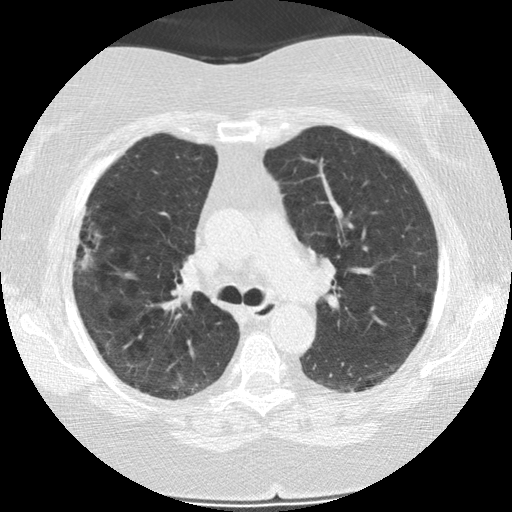
Low-dose screening chest CT, axial slice. Baseline screening round. Lung window (W 1500 / L -600 HU). 2.5 mm slice thickness. Standard (soft-tissue) reconstruction kernel (STANDARD). Slice 69 of 187 in the series. 512 × 512 image matrix. Female participant, aged 73 years at enrolment. Former smoker at enrolment.
Lesion marked by an expert reader, bounding box [x1, y1, x2, y2] px = [60, 208, 108, 275]. Reader record for this screening exam (exam-level; its link to the box is not recorded): non-calcified nodule or mass ≥4 mm, right upper lobe, 21 × 14 mm, poorly defined margins, soft tissue attenuation. Official screen result: positive, change unspecified: nodule(s) >= 4 mm or enlarging nodule(s), mass(es), or other non-specific abnormalities suspicious for lung cancer. Participant outcome: lung cancer diagnosed 482 days after this screen — bronchiolo-alveolar adenocarcinoma, NOS, right upper lobe, moderately differentiated (G2), stage IIIB (AJCC 6th edition), 21 mm at pathology.